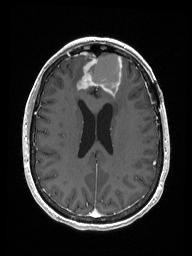
Brain MRI from a brain-tumour surgery series, one axial slice; position 67 of 192 along the scan axis; T1-weighted post-contrast; 192 × 256 image matrix, field of view 187 × 250 mm. From the clinical record (not read from this slice): histopathology: Metastastic Carcinoma from Breast primary; tumour location: Right Frontal.
Outlined on this slice (outlined manually by an expert reader):
- previous resection cavity: bounding box (x1, y1, x2, y2) in pixels: (88, 53, 122, 95)